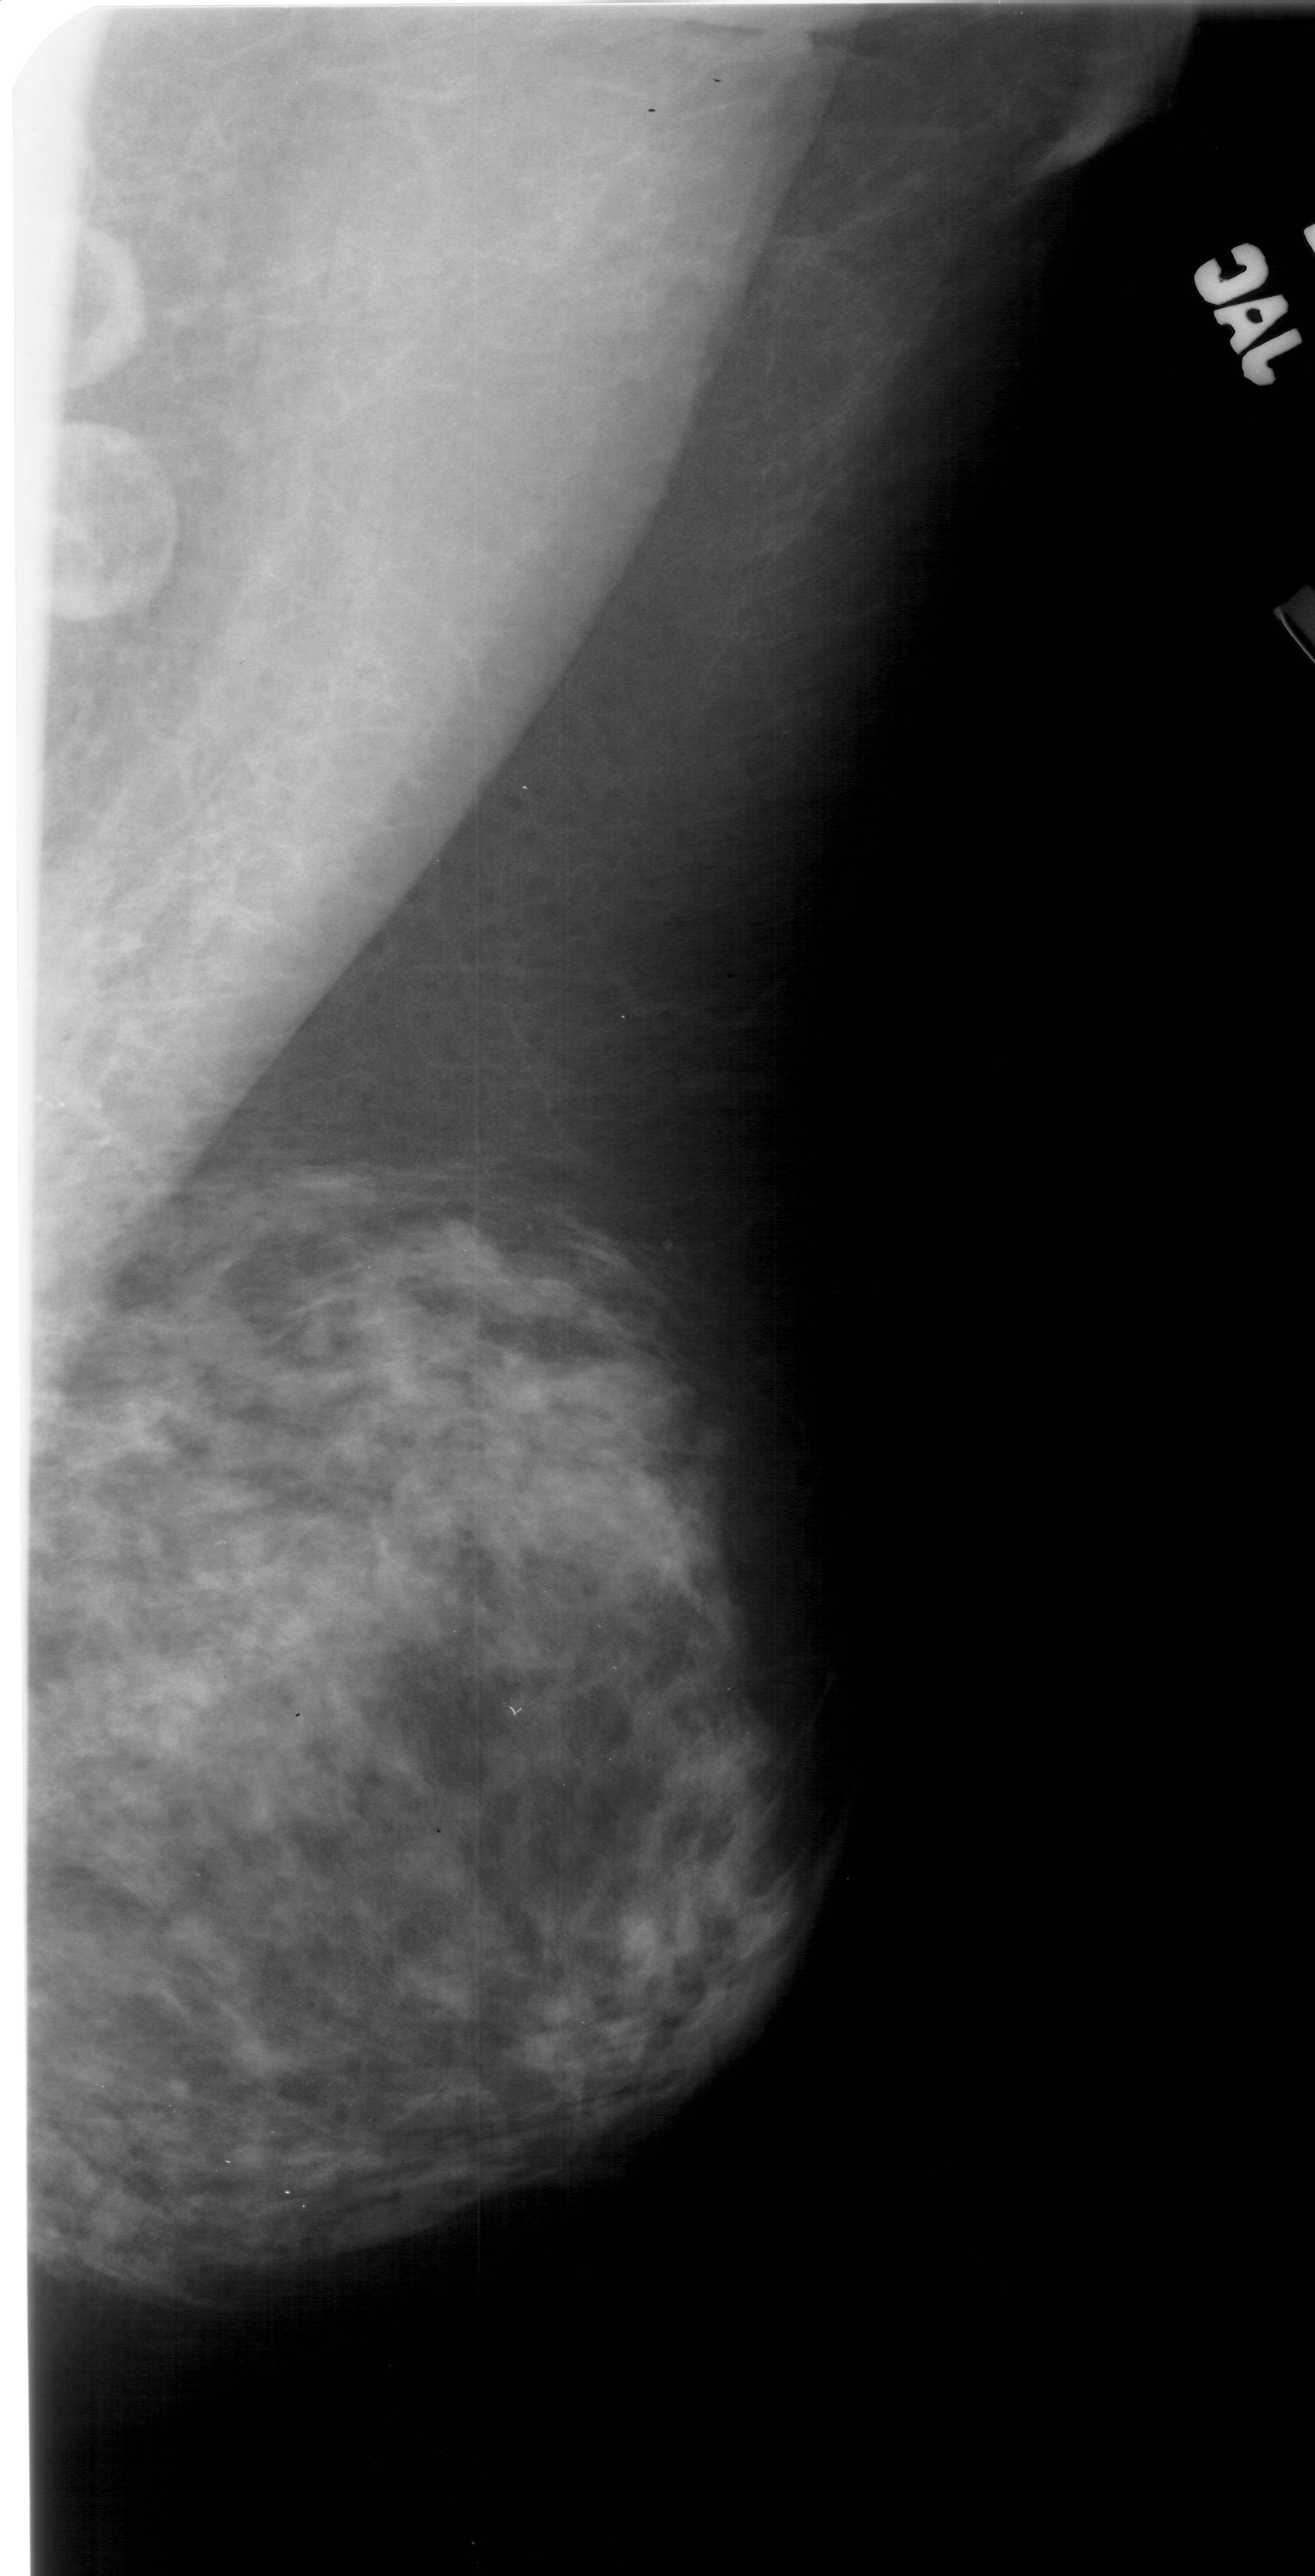
Scanned film-screen mammogram. Right breast. MLO view. Breast composition: heterogeneously dense (BI-RADS density category 3 of 4). 1315 × 2576 image matrix.
Marked abnormalities (boxes around the expert regions of interest):
- calcifications, morphology pleomorphic, distribution clustered; BI-RADS assessment category 4; pathology (as recorded): benign: bounding box [x1, y1, x2, y2] px = [22, 1035, 99, 1140]